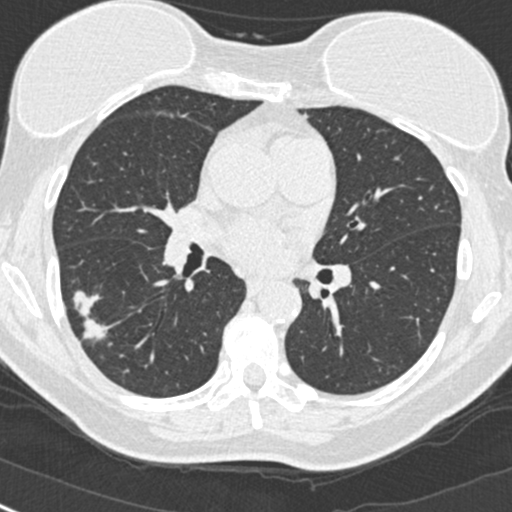
Low-dose screening chest CT, one axial slice; slice 140 of 268 in the series (ordered by position); 120 kVp; lung window (W 1500 / L -600 HU); 1 mm slice thickness; 512 × 512 image matrix, field of view 296 × 296 mm.
Annotated regions visible in this slice (expert manual segmentation):
- lesion 1 (tumor, upper lobe of right lung): bounding box (x1, y1, x2, y2) in pixels: (73, 291, 108, 340)